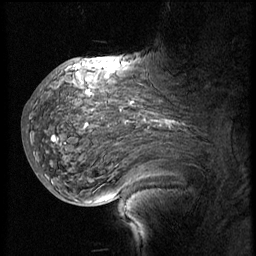
Breast MRI (dynamic contrast-enhanced), one sagittal slice; position 37 of 60 along the scan axis; 3 images stored at this slice position (order not interpretable as contrast timing); 1.5 T; TE 4.2 ms, TR 8.9 ms; 2.5 mm slice thickness; 256 × 256 image matrix. Patient: female, 57 years. From the clinical record (not read from this slice): setting: breast cancer imaged before/during neoadjuvant chemotherapy; receptor status: HER2-positive.
Outlined on this slice (semi-automatically segmented with operator editing):
- analysis volume of interest (the breast-tissue region the enhancement analysis was run in; not a lesion): bounding box (x1, y1, x2, y2) in pixels: (34, 75, 214, 171)
- tumour enhancement mask (voxels above the 140 % enhancement threshold inside the analysis volume of interest): (53, 91, 172, 141)